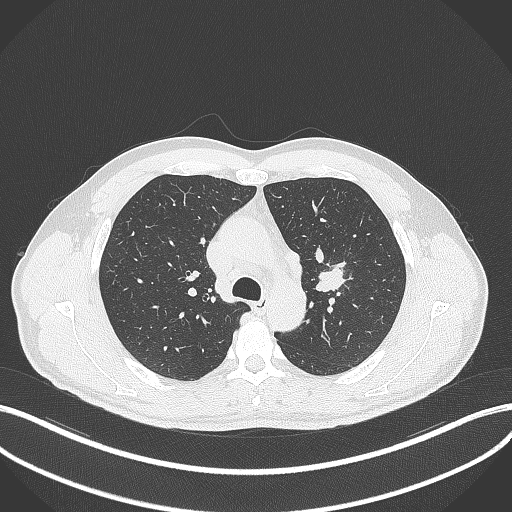
Chest CT, one axial slice. Position 295 of 392 along the scan axis. Reconstruction kernel B70f. 120 kVp. Lung window (W 1500 / L -600 HU). 1 mm slice thickness. 512 × 512 image matrix, field of view 400 × 400 mm. Male patient, age 50 years. Case-level facts recorded for this patient, not image findings: clinical TNM (as recorded): T1c N1 M1b.
Annotated regions visible in this slice (rectangle marked by the reading radiologist):
- lung tumour (recorded histology: squamous cell carcinoma): bounding box <315,266,347,295> (left, top, right, bottom; pixels)